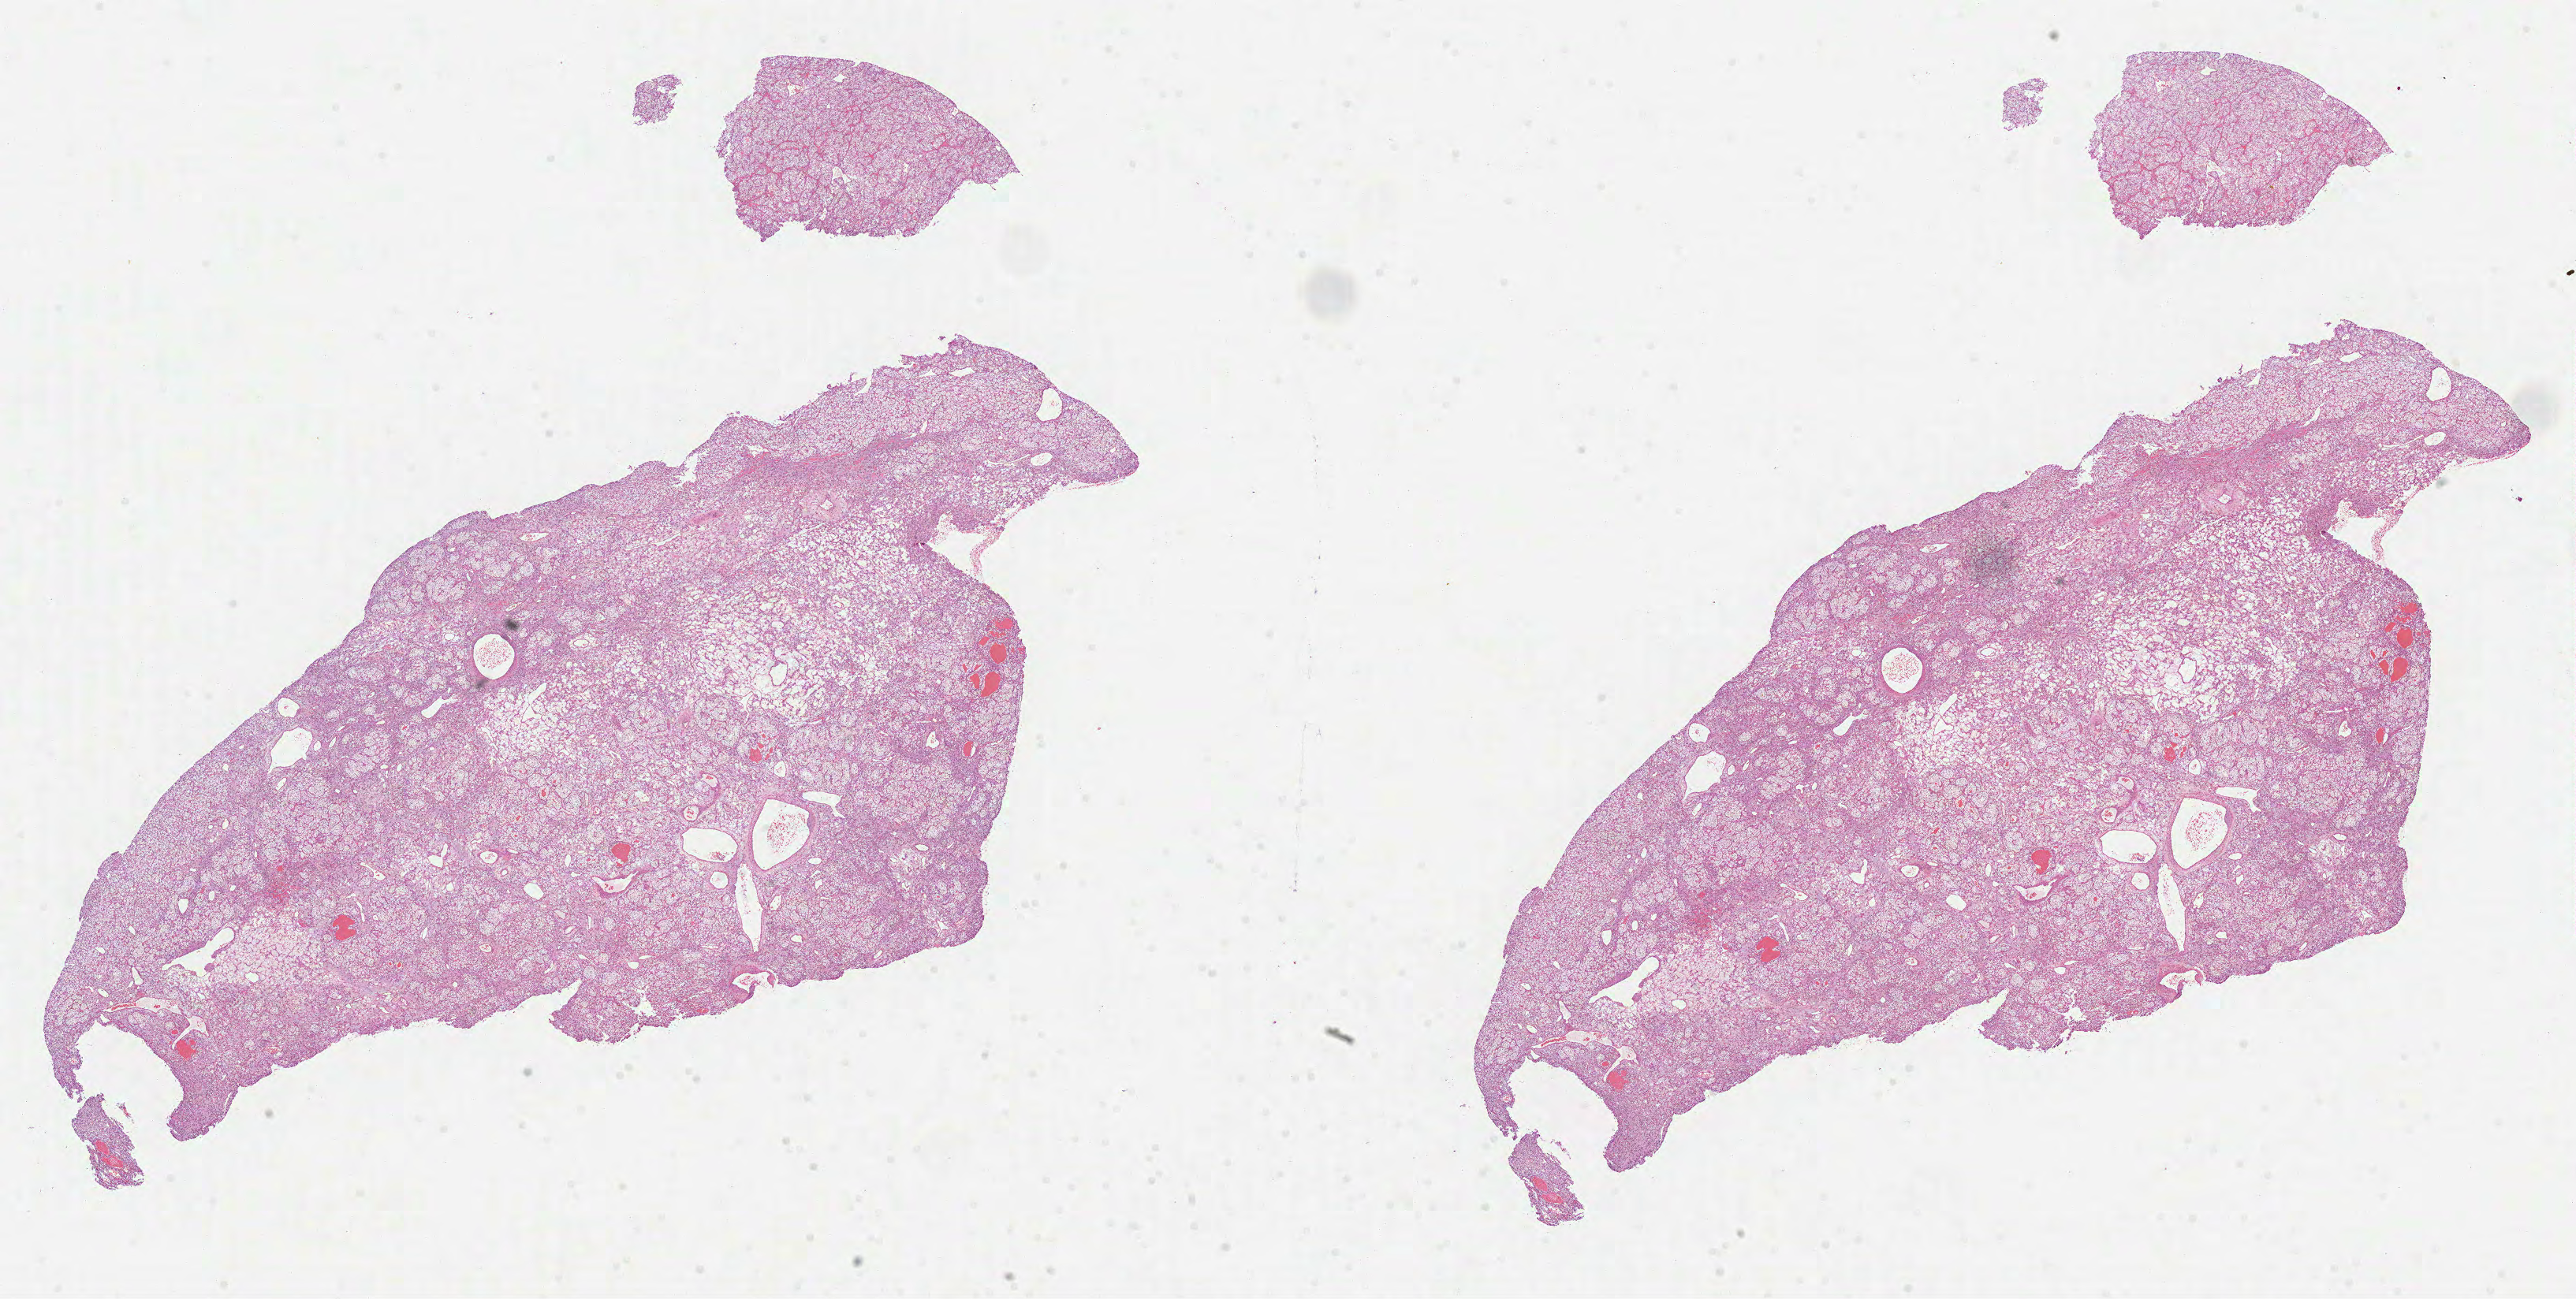
Digitized Hematoxylin and eosin (H&E) stained tissue section (whole slide), low-resolution overview of the scanned area, about 26.3 x 13.3 mm. Formalin-fixed paraffin-embedded (FFPE) diagnostic section. Kidney, primary tumour sample. Patient: female, age at initial diagnosis 34 years. Histologic grade: G2 (moderately differentiated).
Pathologic diagnosis: Clear cell adenocarcinoma, NOS. Laterality: left. AJCC pathologic stage: I.